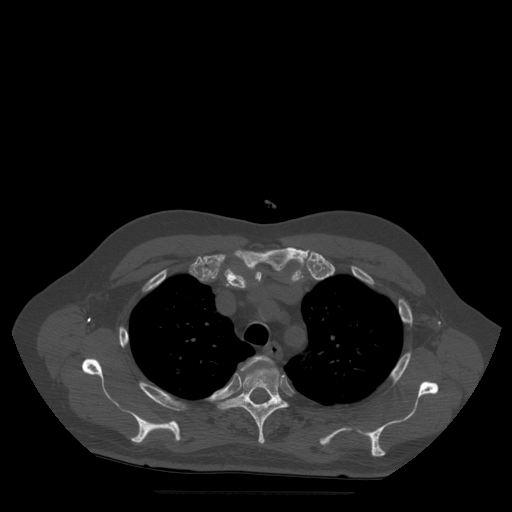
CT including the spine, one axial slice; position 393 of 522 along the scan axis; bone window (W 1800 / L 400 HU); 1.25 mm slice thickness; 512 × 512 image matrix, field of view 420 × 420 mm. Patient age 72 years. From the clinical record (not read from this slice): primary cancer: prostate.
Annotated regions visible in this slice (semi-automatically segmented with operator editing):
- T3 vertebra: bounding box [x1, y1, x2, y2] px = [241, 356, 273, 371]
- T4 vertebra: [219, 367, 288, 444]